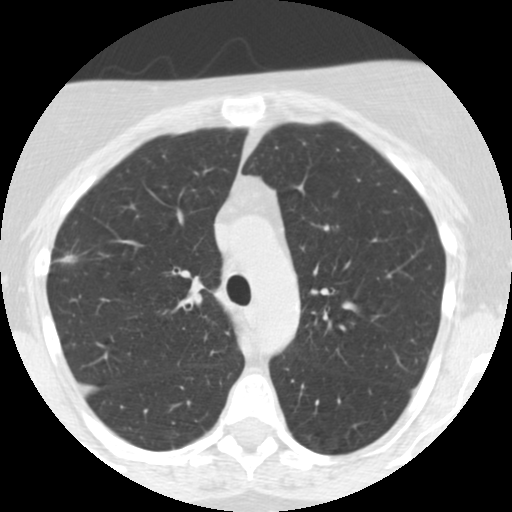
Chest CT (low-dose screening protocol), one axial image; third screening round (two years after baseline); lung window (W 1500 / L -600 HU); 2.5 mm slice thickness; standard (soft-tissue) reconstruction kernel (STANDARD); 120 kVp. Female, age 55 years at enrolment. Current smoker at enrolment.
• Lesion marked by an expert reader, bounding box <45,242,90,281> (left, top, right, bottom; pixels).
• Reader record for this screening exam (exam-level; its link to the box is not recorded): non-calcified nodule or mass ≥4 mm, right upper lobe, 10 × 10 mm, poorly defined margins, soft tissue attenuation, pre-existing on the prior screen: yes; interval growth: yes.
• Lung cancer was diagnosed 145 days after this screen: bronchiolo-alveolar adenocarcinoma, NOS, right upper lobe, moderately differentiated (G2), stage IIA (AJCC 6th edition), 13 mm at pathology.